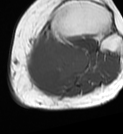
MRI of an extremity soft-tissue mass, one axial slice. Position 42 of 68 along the scan axis. MR volume resampled by the dataset authors to the PET/CT grid (not the native acquisition matrix). 123 × 134 image matrix, field of view 120 × 131 mm. Female patient. From the clinical record (not read from this slice): histological type: extraskeletal high grade osteogenic sarcoma; grade: high; site of the primary tumour: left calf.
Structures marked on this image (expert contour drawn on MRI and transferred to this co-registered scan by the dataset authors):
- gross tumour volume (mass): bounding box <26,36,89,90> (left, top, right, bottom; pixels)